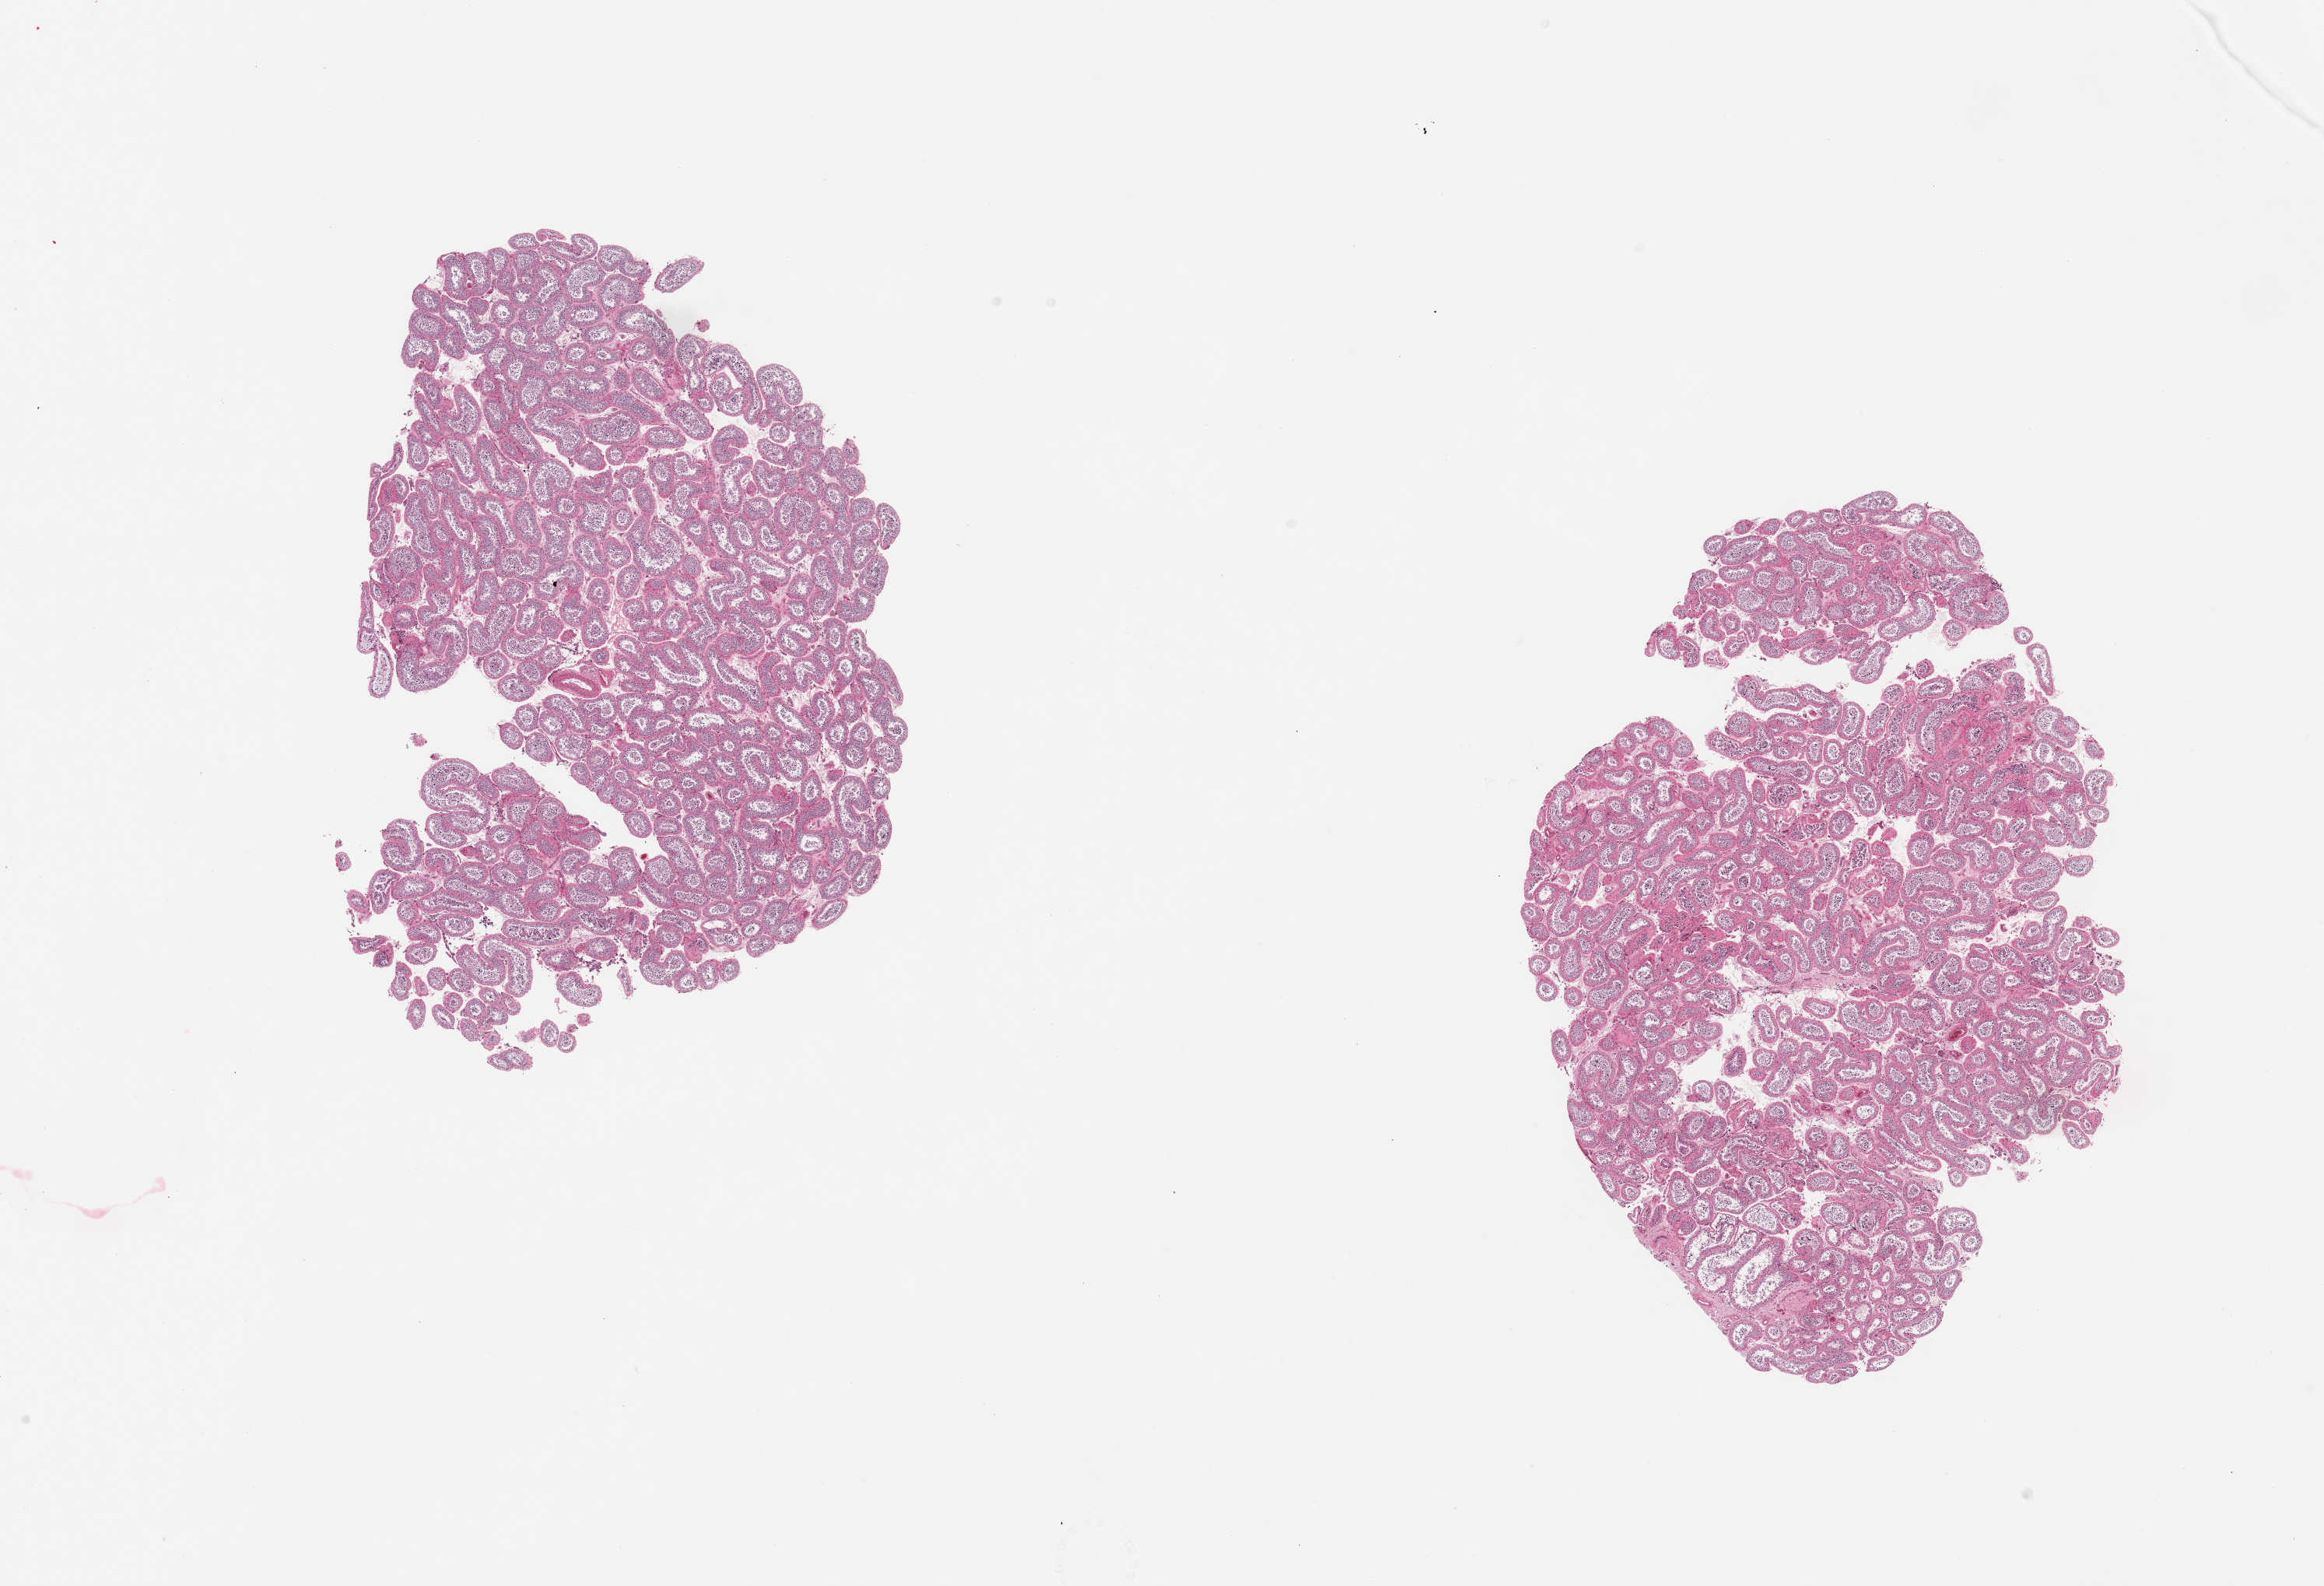
Digitized H&E-stained section — a low-resolution overview of the entire scanned area, about 23.6 x 16.1 mm (slide scanned at 20x); PAXgene-fixed paraffin-embedded (PFPE) section; section of testis (target tissue); donor tissue sample. Donor: male.
Reviewer comment on this tissue sample: 2 pieces; spermatogenesis.